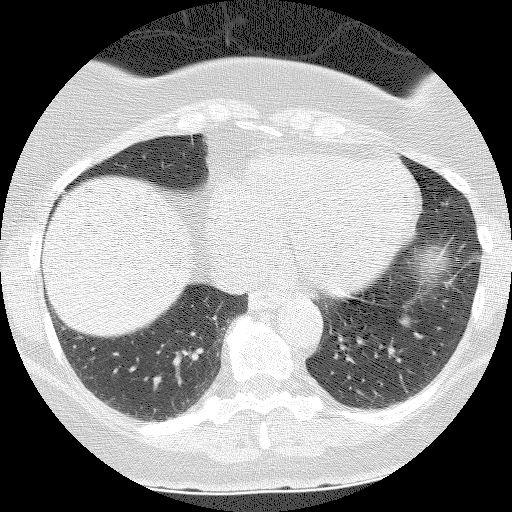
Low-dose screening chest CT, axial slice, second annual screen, lung window (W 1500 / L -600 HU), 120 kVp, 512 × 512 image matrix, field of view 300 × 300 mm. Female participant, aged 55 years at enrolment. Former smoker at enrolment.
Expert reader's lesion annotation, bounding box [x1, y1, x2, y2] px = [380, 304, 429, 348]. The screening reader recorded 3 non-calcified nodules or masses ≥4 mm on this exam; which of them this box marks is not recorded. Official screen result: positive, no significant change: stable abnormalities potentially related to lung cancer, unchanged since the prior screening exam. Lung cancer was diagnosed 655 days after this screen (after the third annual screen): carcinoid tumor, NOS, left lower lobe, carcinoid, stage not assessed, 10 mm at pathology.